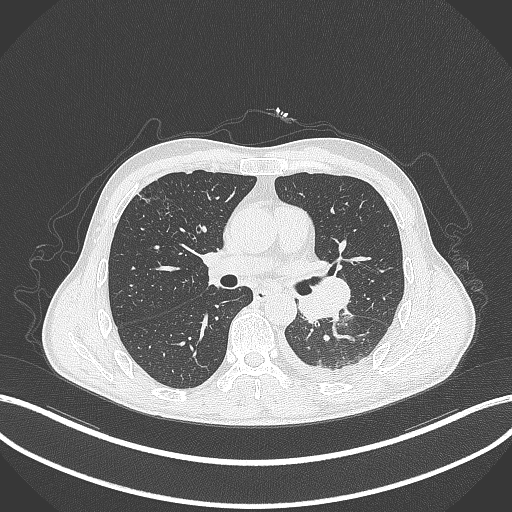
Chest CT, one axial slice. Position 180 of 295 along the scan axis. Reconstruction kernel B70f. 120 kVp. Lung window (W 1500 / L -600 HU). 512 × 512 image matrix. Male patient, age 47 years. From the clinical record (not read from this slice): clinical TNM (as recorded): T3 N1 M1c.
Structures marked on this image (rectangle marked by the reading radiologist):
- lung tumour (recorded histology: small cell carcinoma): bounding box (x1, y1, x2, y2) in pixels: (295, 274, 353, 329)